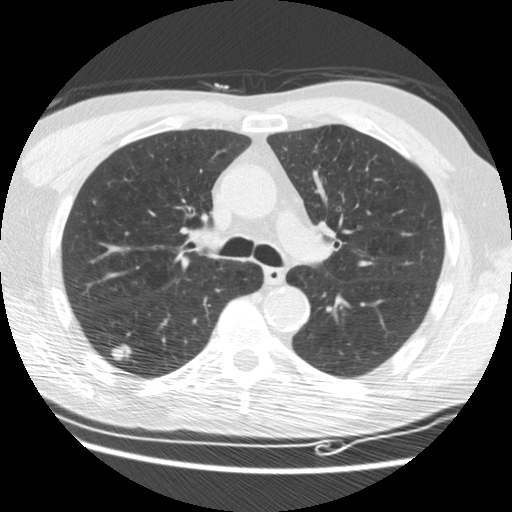
Chest CT (low-dose screening protocol), one axial image. Third annual screen. Lung window (W 1500 / L -600 HU). Standard (soft-tissue) reconstruction kernel (STANDARD). 120 kVp. Male, age 62 years at enrolment. Current smoker at enrolment.
• Lesion marked by an expert reader, bounding box (x1, y1, x2, y2) in pixels: (103, 334, 141, 368).
• The screening reader recorded 3 non-calcified nodules or masses ≥4 mm on this exam; which of them this box marks is not recorded.
• Later outcome: lung cancer diagnosed 33 days after this screen — adenocarcinoma, NOS, right lower lobe, moderately differentiated (G2), stage IIIB (AJCC 6th edition), 15 mm at pathology.